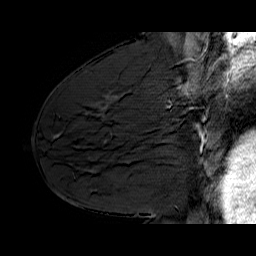
Breast MRI (dynamic contrast-enhanced), one sagittal slice; slice 33 of 60 in the series (ordered by position); dynamic contrast-enhanced series, time point 2 of 6 at this slice position (early post-contrast); 1.5 T; TE 6.4 ms, TR 32.9 ms; 4 mm slice thickness; 256 × 256 image matrix. Female patient. Case-level facts recorded for this patient, not image findings: setting: breast cancer imaged before/during neoadjuvant chemotherapy; receptor status: HER2-positive.
Structures marked on this image (semi-automatically segmented with operator editing):
- analysis volume of interest (the breast-tissue region the enhancement analysis was run in; not a lesion): bounding box (x1, y1, x2, y2) in pixels: (132, 62, 210, 128)
- tumour enhancement mask (voxels above the 100 % enhancement threshold inside the analysis volume of interest): (183, 80, 194, 95)